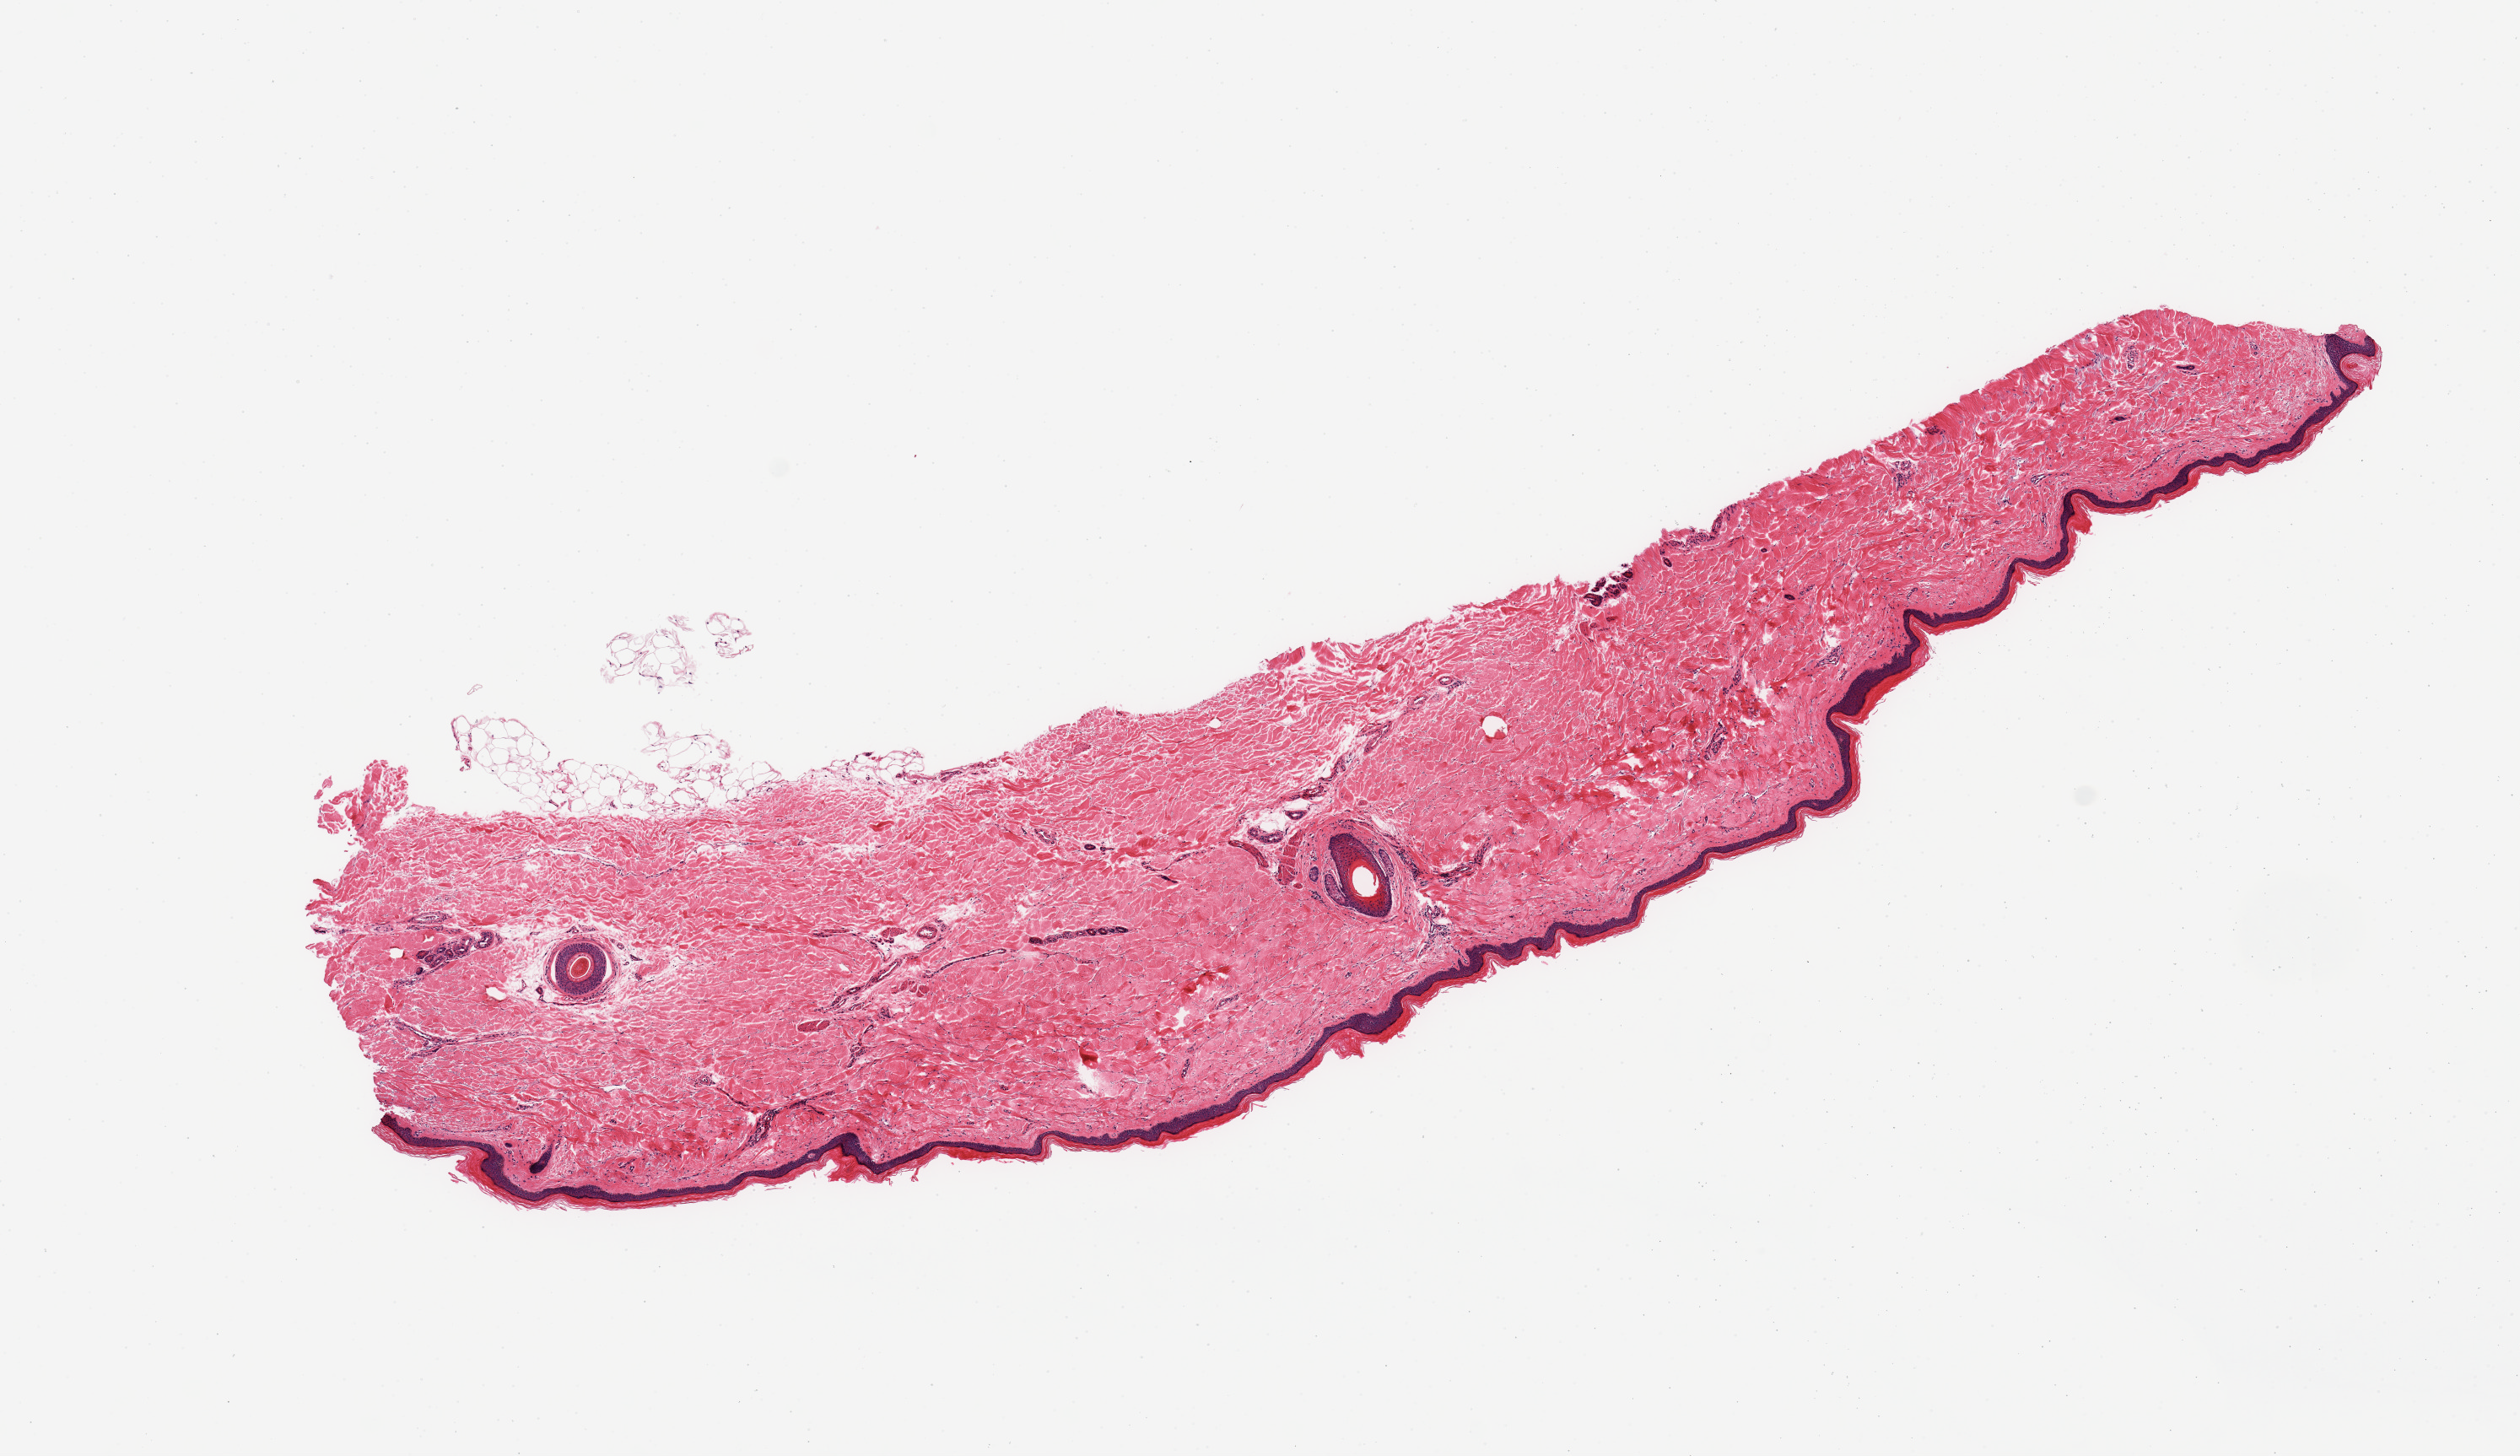
Haematoxylin and eosin whole-slide image, brightfield, a low-resolution overview of the entire scanned area, about 11.8 x 6.8 mm; PAXgene-fixed, paraffin-embedded tissue; target tissue: skin of lower leg; tissue donor sample. Donor: male.
Review note (as recorded): 1 piece; not adipose tissue, skin.